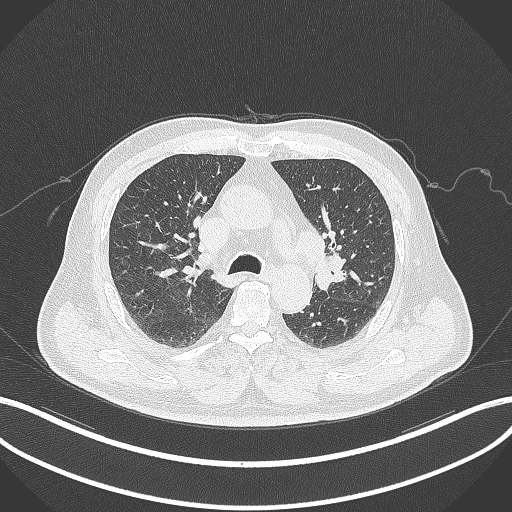
Chest CT, one axial slice; 120 kVp; lung window (W 1500 / L -600 HU); 1 mm slice thickness; 512 × 512 image matrix, field of view 400 × 400 mm. Patient: male, 67 years. Case-level facts recorded for this patient, not image findings: clinical TNM (as recorded): T2a N1 M0; histopathological grade: G3.
Annotated regions visible in this slice (bounding box drawn by a radiologist):
- lung tumour (recorded histology: adenocarcinoma): bounding box [x1, y1, x2, y2] px = [311, 252, 351, 292]